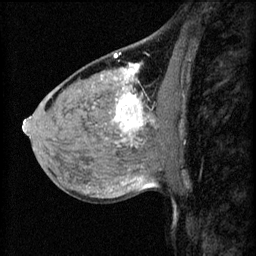
Breast MRI (dynamic contrast-enhanced), one sagittal slice. Position 35 of 60 along the scan axis. 3 images stored at this slice position (order not interpretable as contrast timing). 1.5 T. TE 4.2 ms, TR 8.2 ms. 2.2 mm slice thickness. 256 × 256 image matrix, field of view 180 × 180 mm. Patient: female, 40 years.
Annotated regions visible in this slice (semi-automatically segmented with operator editing):
- analysis volume of interest (the breast-tissue region the enhancement analysis was run in; not a lesion): bounding box (x1, y1, x2, y2) in pixels: (108, 82, 175, 139)
- tumour enhancement mask (voxels above the 70 % enhancement threshold inside the analysis volume of interest): (114, 82, 147, 135)